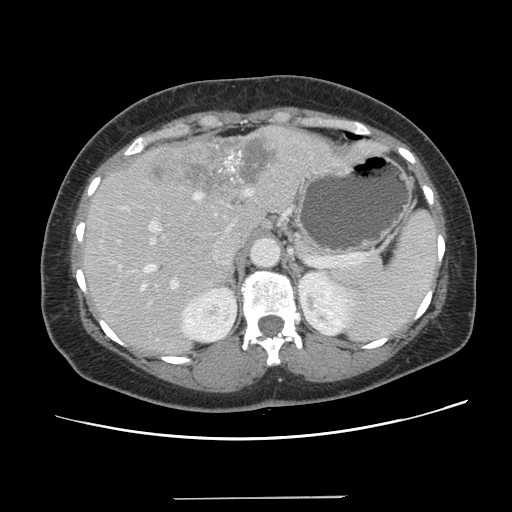
Contrast-enhanced abdominal CT, one axial slice. Position 91 of 141 along the scan axis. 120 kVp. Intravenous contrast given. Soft-tissue window (W 400 / L 40 HU). 512 × 512 image matrix. Female patient, age 53 years. Case-level facts recorded for this patient, not image findings: diagnosis: colorectal cancer liver metastases, imaged before liver resection; multiple liver metastases: no; largest metastasis: 14.5 cm.
Annotated regions visible in this slice (outlined manually by an expert reader):
- hepatic veins: box from (x=141, y=193) to (x=201, y=289) px
- liver: (x=85, y=127)–(x=380, y=354)
- planned liver remnant (the part of the liver to remain after resection): (x=84, y=208)–(x=263, y=354)
- portal vein (with intrahepatic branches): (x=149, y=189)–(x=251, y=292)
- liver metastasis: (x=149, y=137)–(x=276, y=194)